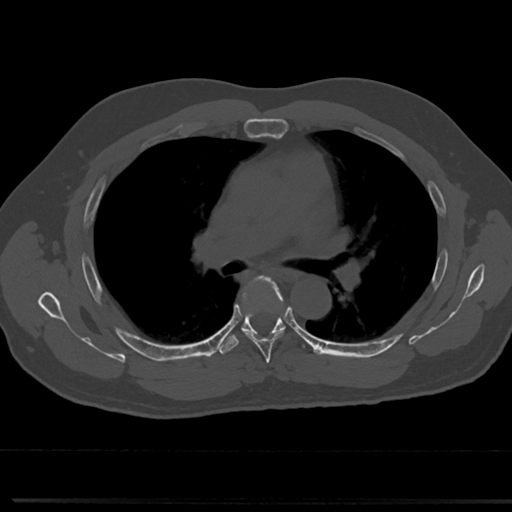
CT including the spine, one axial slice; slice 479 of 817 in the series (ordered by position); reconstruction kernel Br40s/3; 120 kVp; bone window (W 1800 / L 400 HU); 512 × 512 image matrix, field of view 355 × 355 mm. Patient: male, 61 years. From the clinical record (not read from this slice): primary cancer: prostate.
Outlined on this slice (semi-automatically segmented with operator editing):
- T5 vertebra: bounding box <238,277,288,359> (left, top, right, bottom; pixels)
- T6 vertebra: <240,324,287,335>